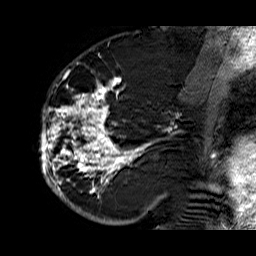
Breast MRI (dynamic contrast-enhanced), one sagittal slice; position 35 of 60 along the scan axis; dynamic contrast-enhanced series, time point 2 of 6 at this slice position (early post-contrast); 1.5 T; TE 6.3 ms, TR 32.9 ms; 256 × 256 image matrix, field of view 200 × 200 mm. Female patient. Case-level facts recorded for this patient, not image findings: setting: breast cancer imaged before/during neoadjuvant chemotherapy; receptor status: HR-positive, HER2-negative.
Structures marked on this image (semi-automatically segmented with operator editing):
- analysis volume of interest (the breast-tissue region the enhancement analysis was run in; not a lesion): bounding box (x1, y1, x2, y2) in pixels: (39, 74, 176, 210)
- tumour enhancement mask (voxels above the 100 % enhancement threshold inside the analysis volume of interest): (39, 75, 153, 210)